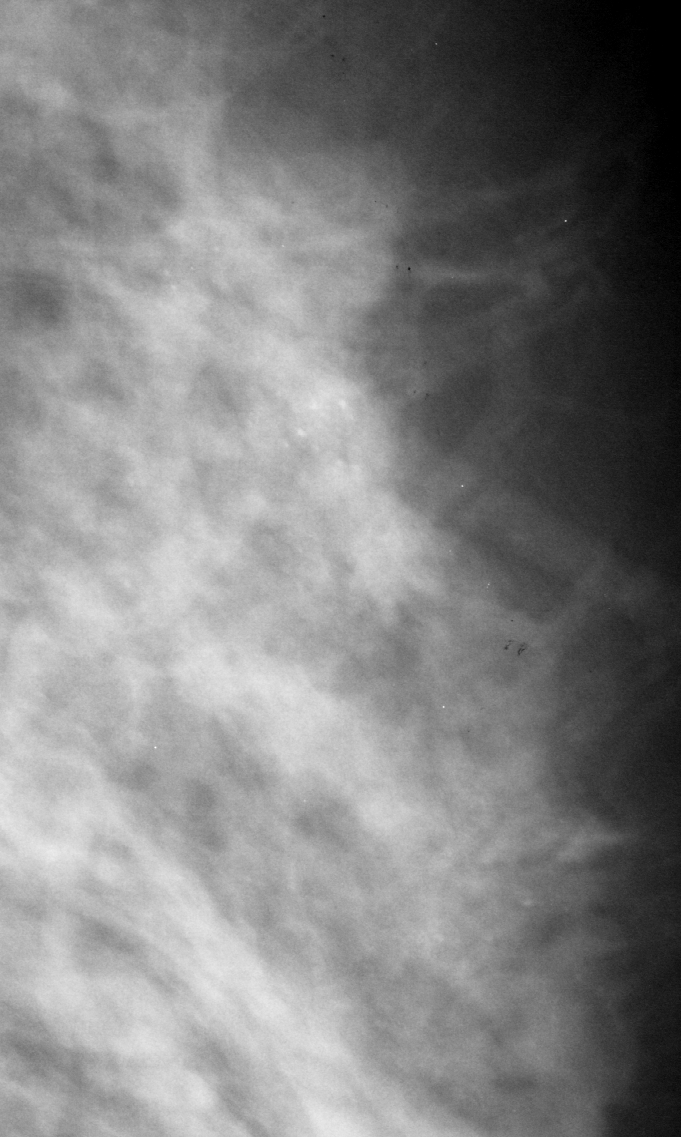
Cropped region of a digitized screen-film mammogram centred on a radiologist-marked abnormality, left breast, MLO view, BI-RADS breast density category 2 (scale 1–4).
Marked abnormality: calcifications, morphology amorphous, distribution regional; BI-RADS assessment category 4; subtlety rating 3 on a 1 (subtle) to 5 (obvious) scale; pathology (as recorded): malignant.